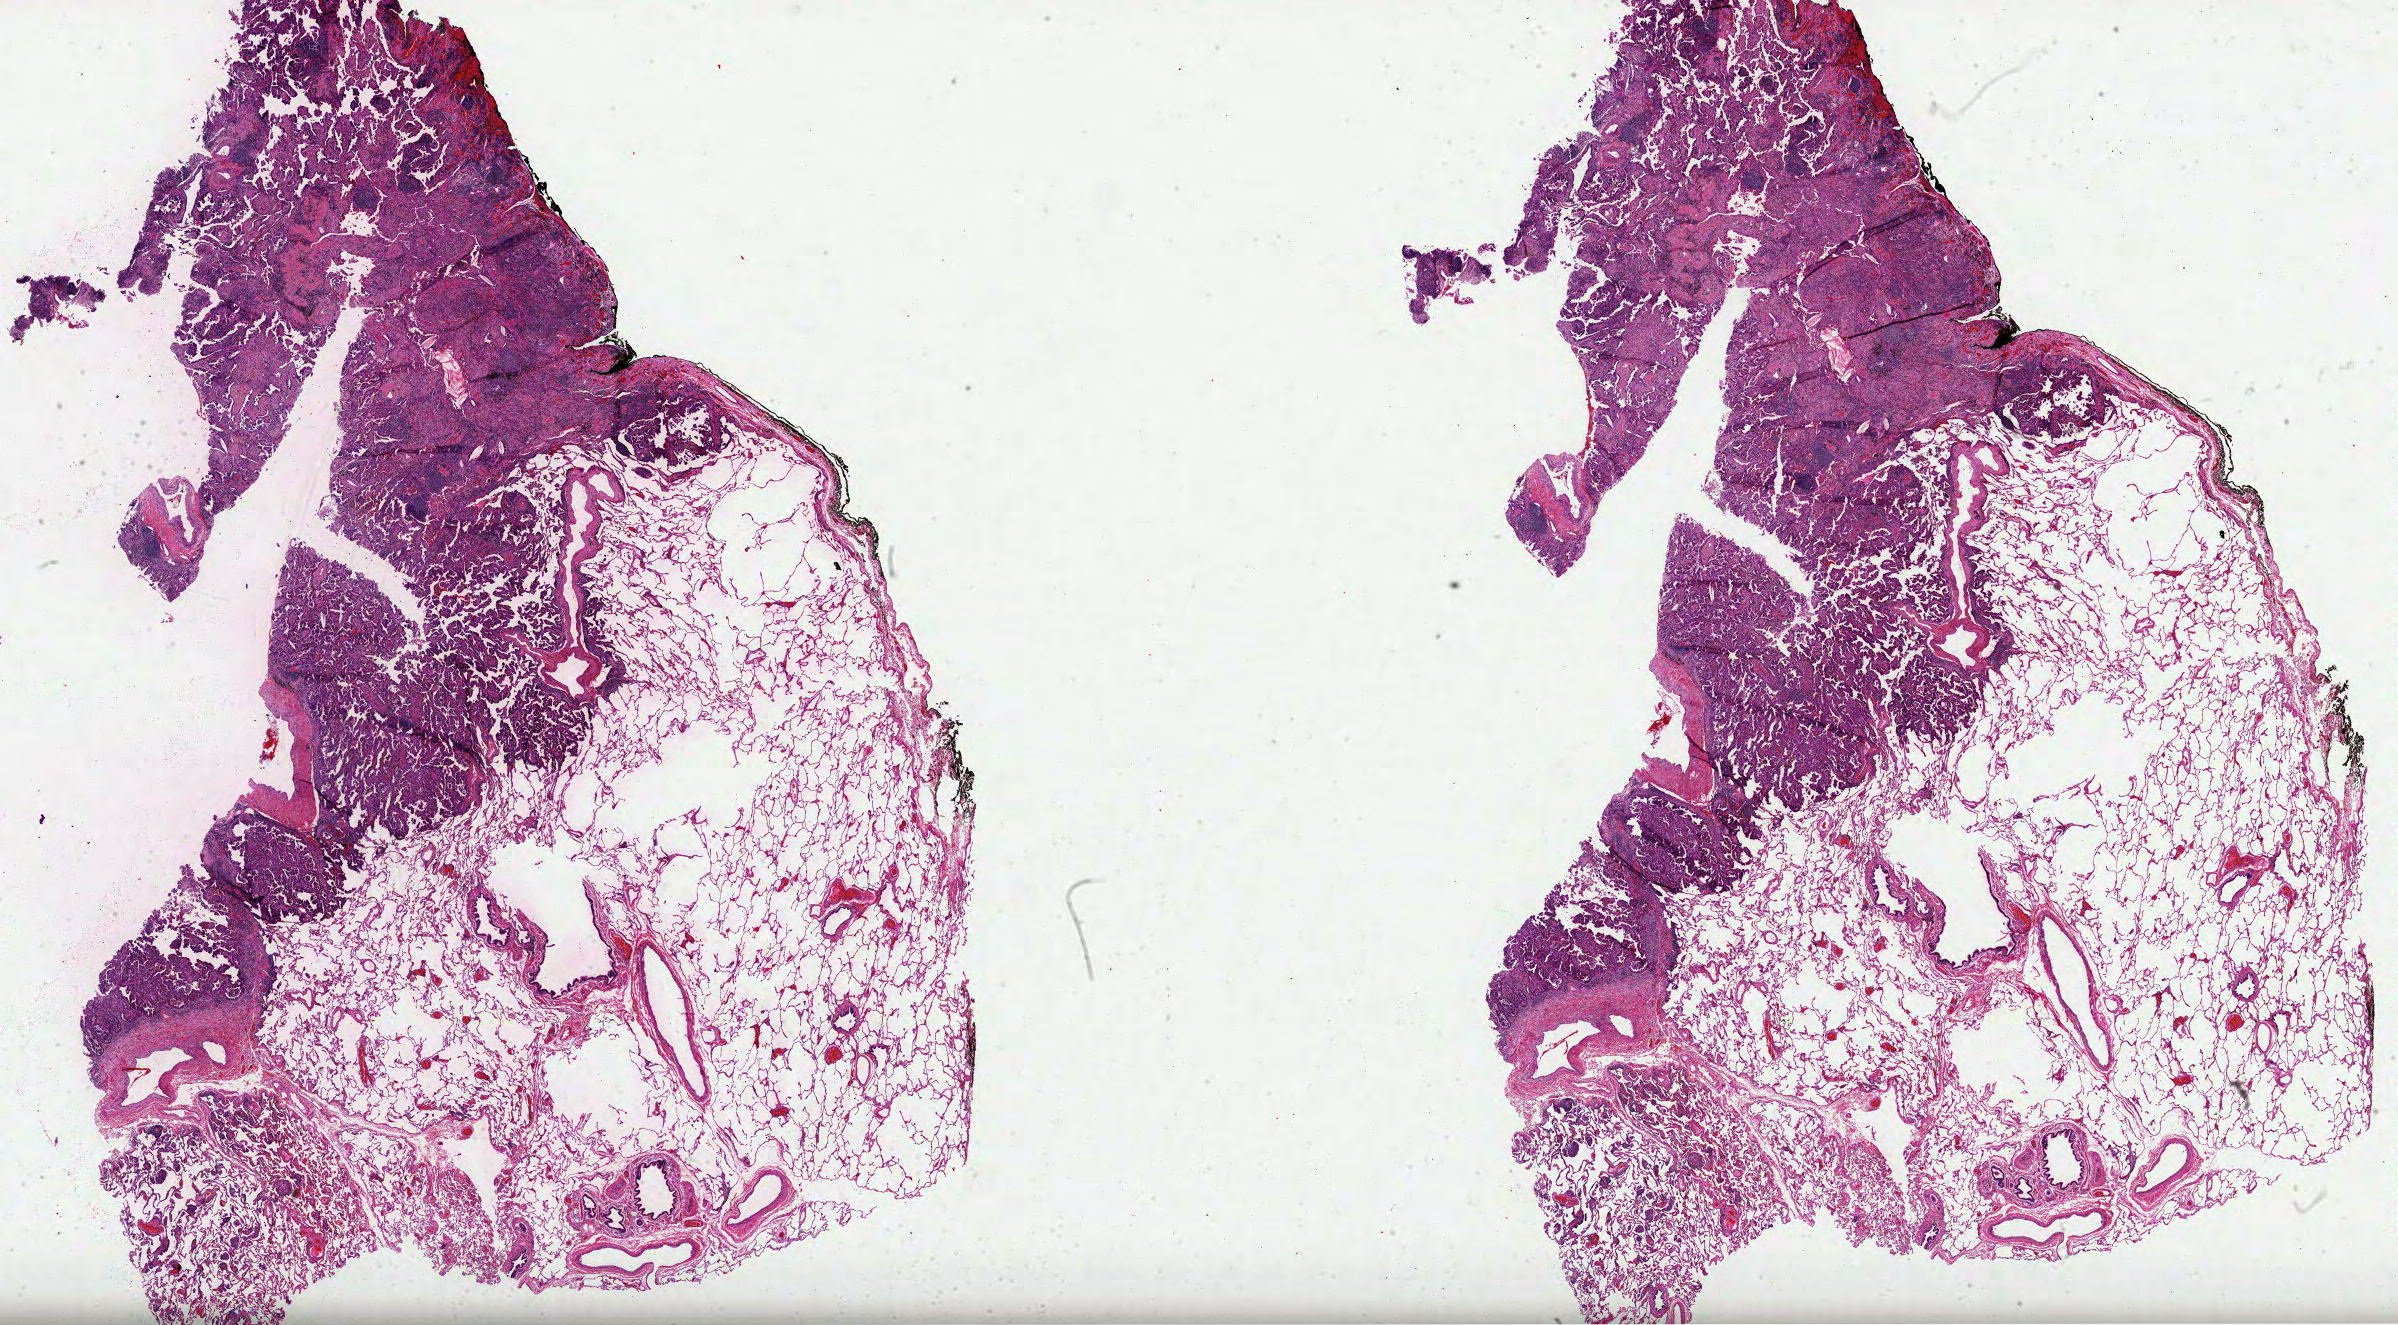
Digitized H&E tissue section (whole slide) — a low-resolution overview of the entire scanned area, about 38.7 x 21.4 mm, formalin-fixed paraffin-embedded (FFPE) diagnostic section, lung, primary tumour sample. Female patient; age at initial diagnosis 74 years.
AJCC pathologic stage: IA (3rd edition). Pathologic diagnosis: Adenocarcinoma, NOS (lower lobe, lung).